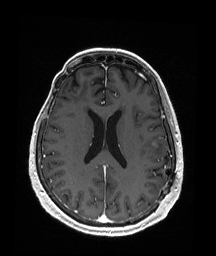
Brain MRI from a brain-tumour surgery series, one axial slice. Position 78 of 176 along the scan axis. T1-weighted post-contrast. 1 mm slice thickness. 216 × 256 image matrix, field of view 211 × 250 mm. From the clinical record (not read from this slice): histopathology: Metastatic Malignant Melanoma; tumour location: Left Frontal.
Structures marked on this image (outlined manually by an expert reader):
- tumour: bounding box (x1, y1, x2, y2) in pixels: (153, 143, 158, 147)